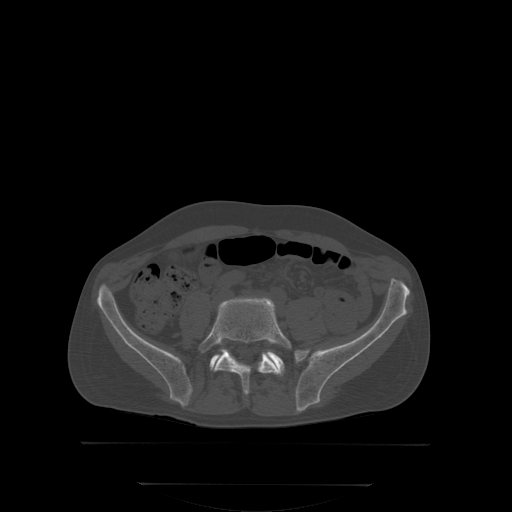
CT including the spine, one axial slice; position 94 of 350 along the scan axis; bone window (W 1800 / L 400 HU); 512 × 512 image matrix. Patient: male, 58 years. From the clinical record (not read from this slice): primary cancer: prostate; vertebrae with lytic lesions (as recorded): L1.
Annotated regions visible in this slice (semi-automatic segmentation, software-assisted and operator-edited):
- L5 vertebra: bounding box <200,298,290,393> (left, top, right, bottom; pixels)